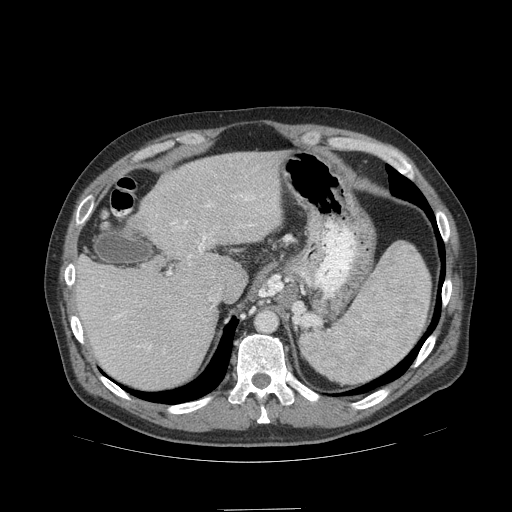
Contrast-enhanced abdominal CT (liver protocol), one axial slice. Position 76 of 99 along the scan axis. 140 kVp. Soft-tissue window (W 400 / L 40 HU). 2.5 mm slice thickness. 512 × 512 image matrix, field of view 440 × 440 mm. From the clinical record (not read from this slice): diagnosis: hepatocellular carcinoma (patient treated with transarterial chemoembolisation; whether this scan precedes or follows treatment is not stated here); TNM stage (as recorded): Stage-I; Child-Pugh class: A; tumour differentiation: no biopsy; tumour nodularity: uninodular.
Structures marked on this image (semi-automatic segmentation, software-assisted and operator-edited):
- liver parenchyma outside the tumour (the mass and vessels are separate outlines, so this box may not span the whole liver): bounding box (x1, y1, x2, y2) in pixels: (72, 150, 285, 388)
- liver vessels: (73, 194, 265, 350)